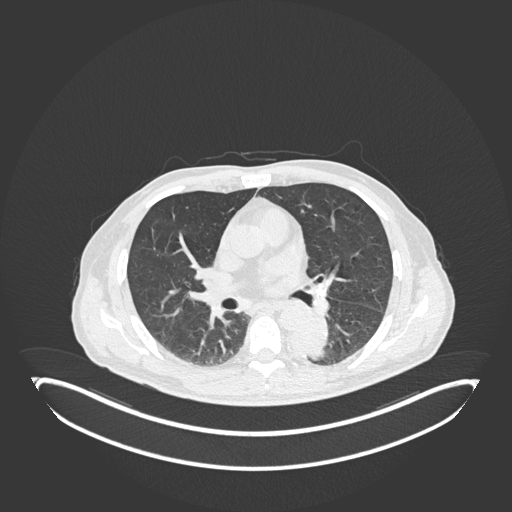
Chest CT, one axial slice; slice 109 of 251 in the series (ordered by position); reconstruction kernel B30f; lung window (W 1500 / L -600 HU); 1 mm slice thickness; 512 × 512 image matrix. Male patient, age 72 years. Case-level facts recorded for this patient, not image findings: clinical TNM (as recorded): T2b N0 M1.
Annotated regions visible in this slice (bounding box drawn by a radiologist):
- lung tumour (recorded histology: adenocarcinoma): bounding box [x1, y1, x2, y2] px = [284, 311, 330, 362]